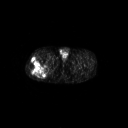
FDG PET of an extremity soft-tissue mass (from a PET/CT study), one axial slice. Slice 263 of 267 in the series (ordered by position). 128 × 128 image matrix. Male patient, age 43 years. Case-level facts recorded for this patient, not image findings: histological type: poorly differentiated synovial sarcoma; grade: high; site of the primary tumour: right buttock.
Structures marked on this image (expert contour drawn on MRI and transferred to this co-registered scan by the dataset authors):
- gross tumour volume including surrounding oedema: bounding box (x1, y1, x2, y2) in pixels: (28, 58, 50, 78)
- gross tumour volume (mass): (28, 58, 48, 78)